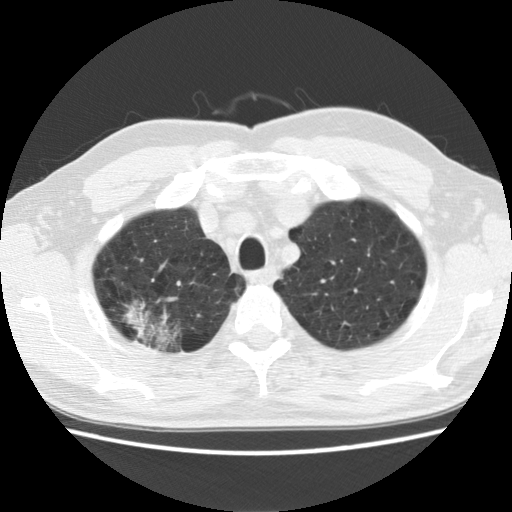
Chest CT (low-dose screening protocol), one axial image, baseline annual screen, lung window (W 1500 / L -600 HU), 2.5 mm slice thickness. Male participant, aged 64 years at enrolment.
Lesion marked by an expert reader, bounding box (x1, y1, x2, y2) in pixels: (108, 289, 196, 362). Reader record for this screening exam (exam-level; its link to the box is not recorded): non-calcified nodule or mass ≥4 mm, right upper lobe, 39 × 31 mm, spiculated (stellate) margins, mixed attenuation. Participant outcome: lung cancer diagnosed 74 days after this screen — adenocarcinoma, NOS, right upper lobe, moderately differentiated (G2), stage IB (AJCC 6th edition), 40 mm at pathology.